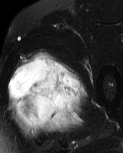
MRI of an extremity soft-tissue mass, one axial slice; position 38 of 60 along the scan axis; T2-weighted fat-saturated; MR volume resampled by the dataset authors to the PET/CT grid (not the native acquisition matrix); 3.27 mm slice thickness; 123 × 153 image matrix, field of view 120 × 149 mm. Male patient. From the clinical record (not read from this slice): histological type: pleiomorphic liposarcoma; grade: high; site of the primary tumour: left thigh.
Outlined on this slice (expert contour drawn on MRI and transferred to this co-registered scan by the dataset authors):
- gross tumour volume including surrounding oedema: bounding box <8,49,87,140> (left, top, right, bottom; pixels)
- gross tumour volume (mass): <8,54,85,128>